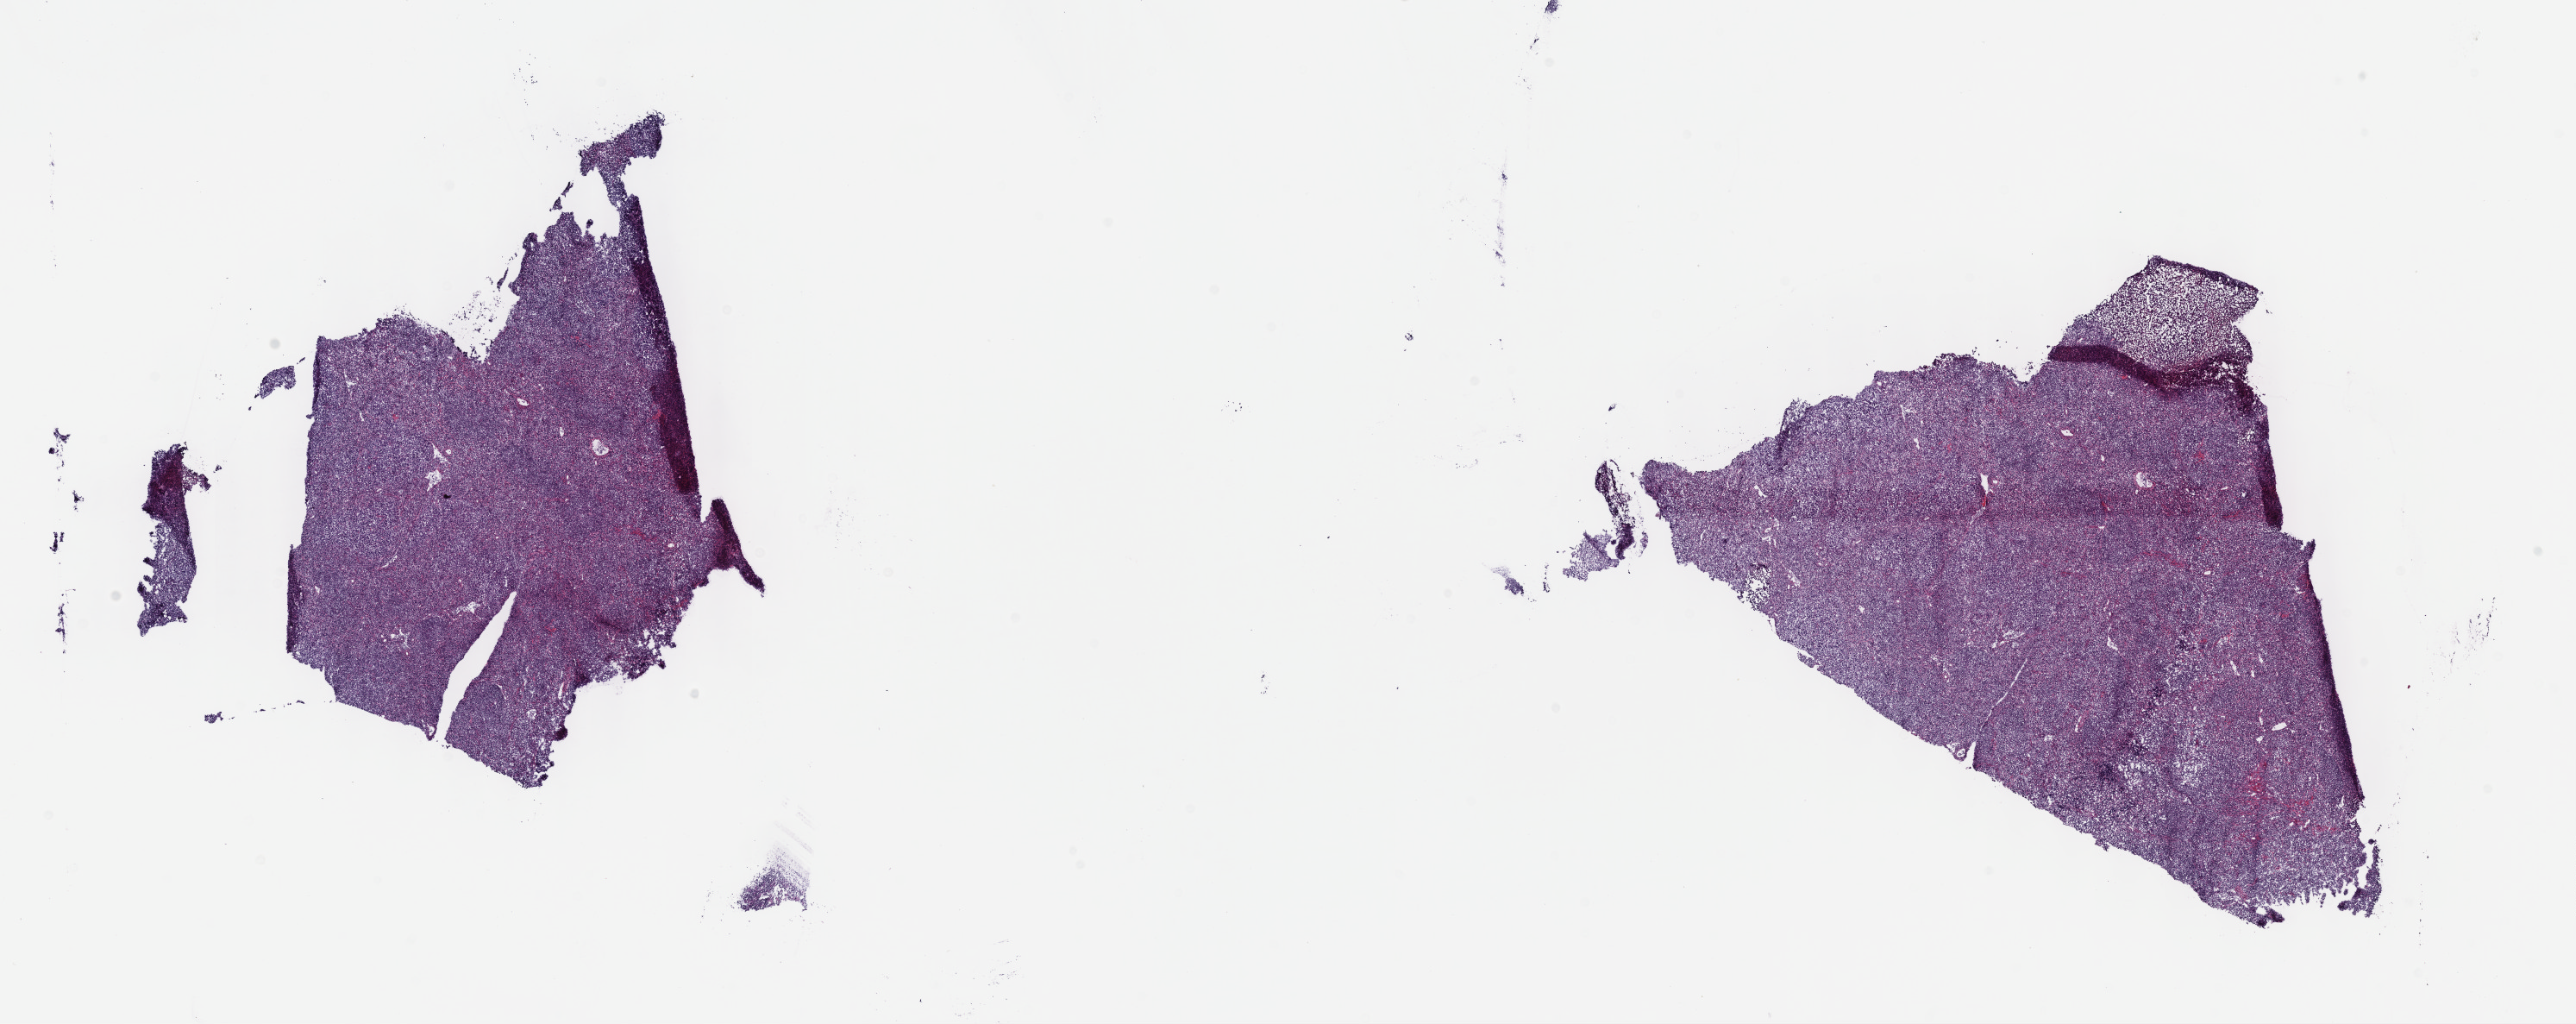
Hematoxylin and eosin (H&E) stained whole-slide image — low-resolution overview of the scanned area, about 24.2 x 9.6 mm (acquisition: 40x scan); frozen section; sample: primary tumour, lymphoid tissue. Female, age 64 years at initial diagnosis. Slide review estimates, as recorded: tumour cells 80%, tumour nuclei 90%, normal cells 10%, stromal cells 5%, necrosis 5%. Inflammatory infiltration, as recorded: lymphocyte infiltration 80%, monocyte infiltration 10%, neutrophil infiltration 5%.
* pathologic diagnosis: Diffuse large B-cell lymphoma, NOS (lymph nodes of axilla or arm)